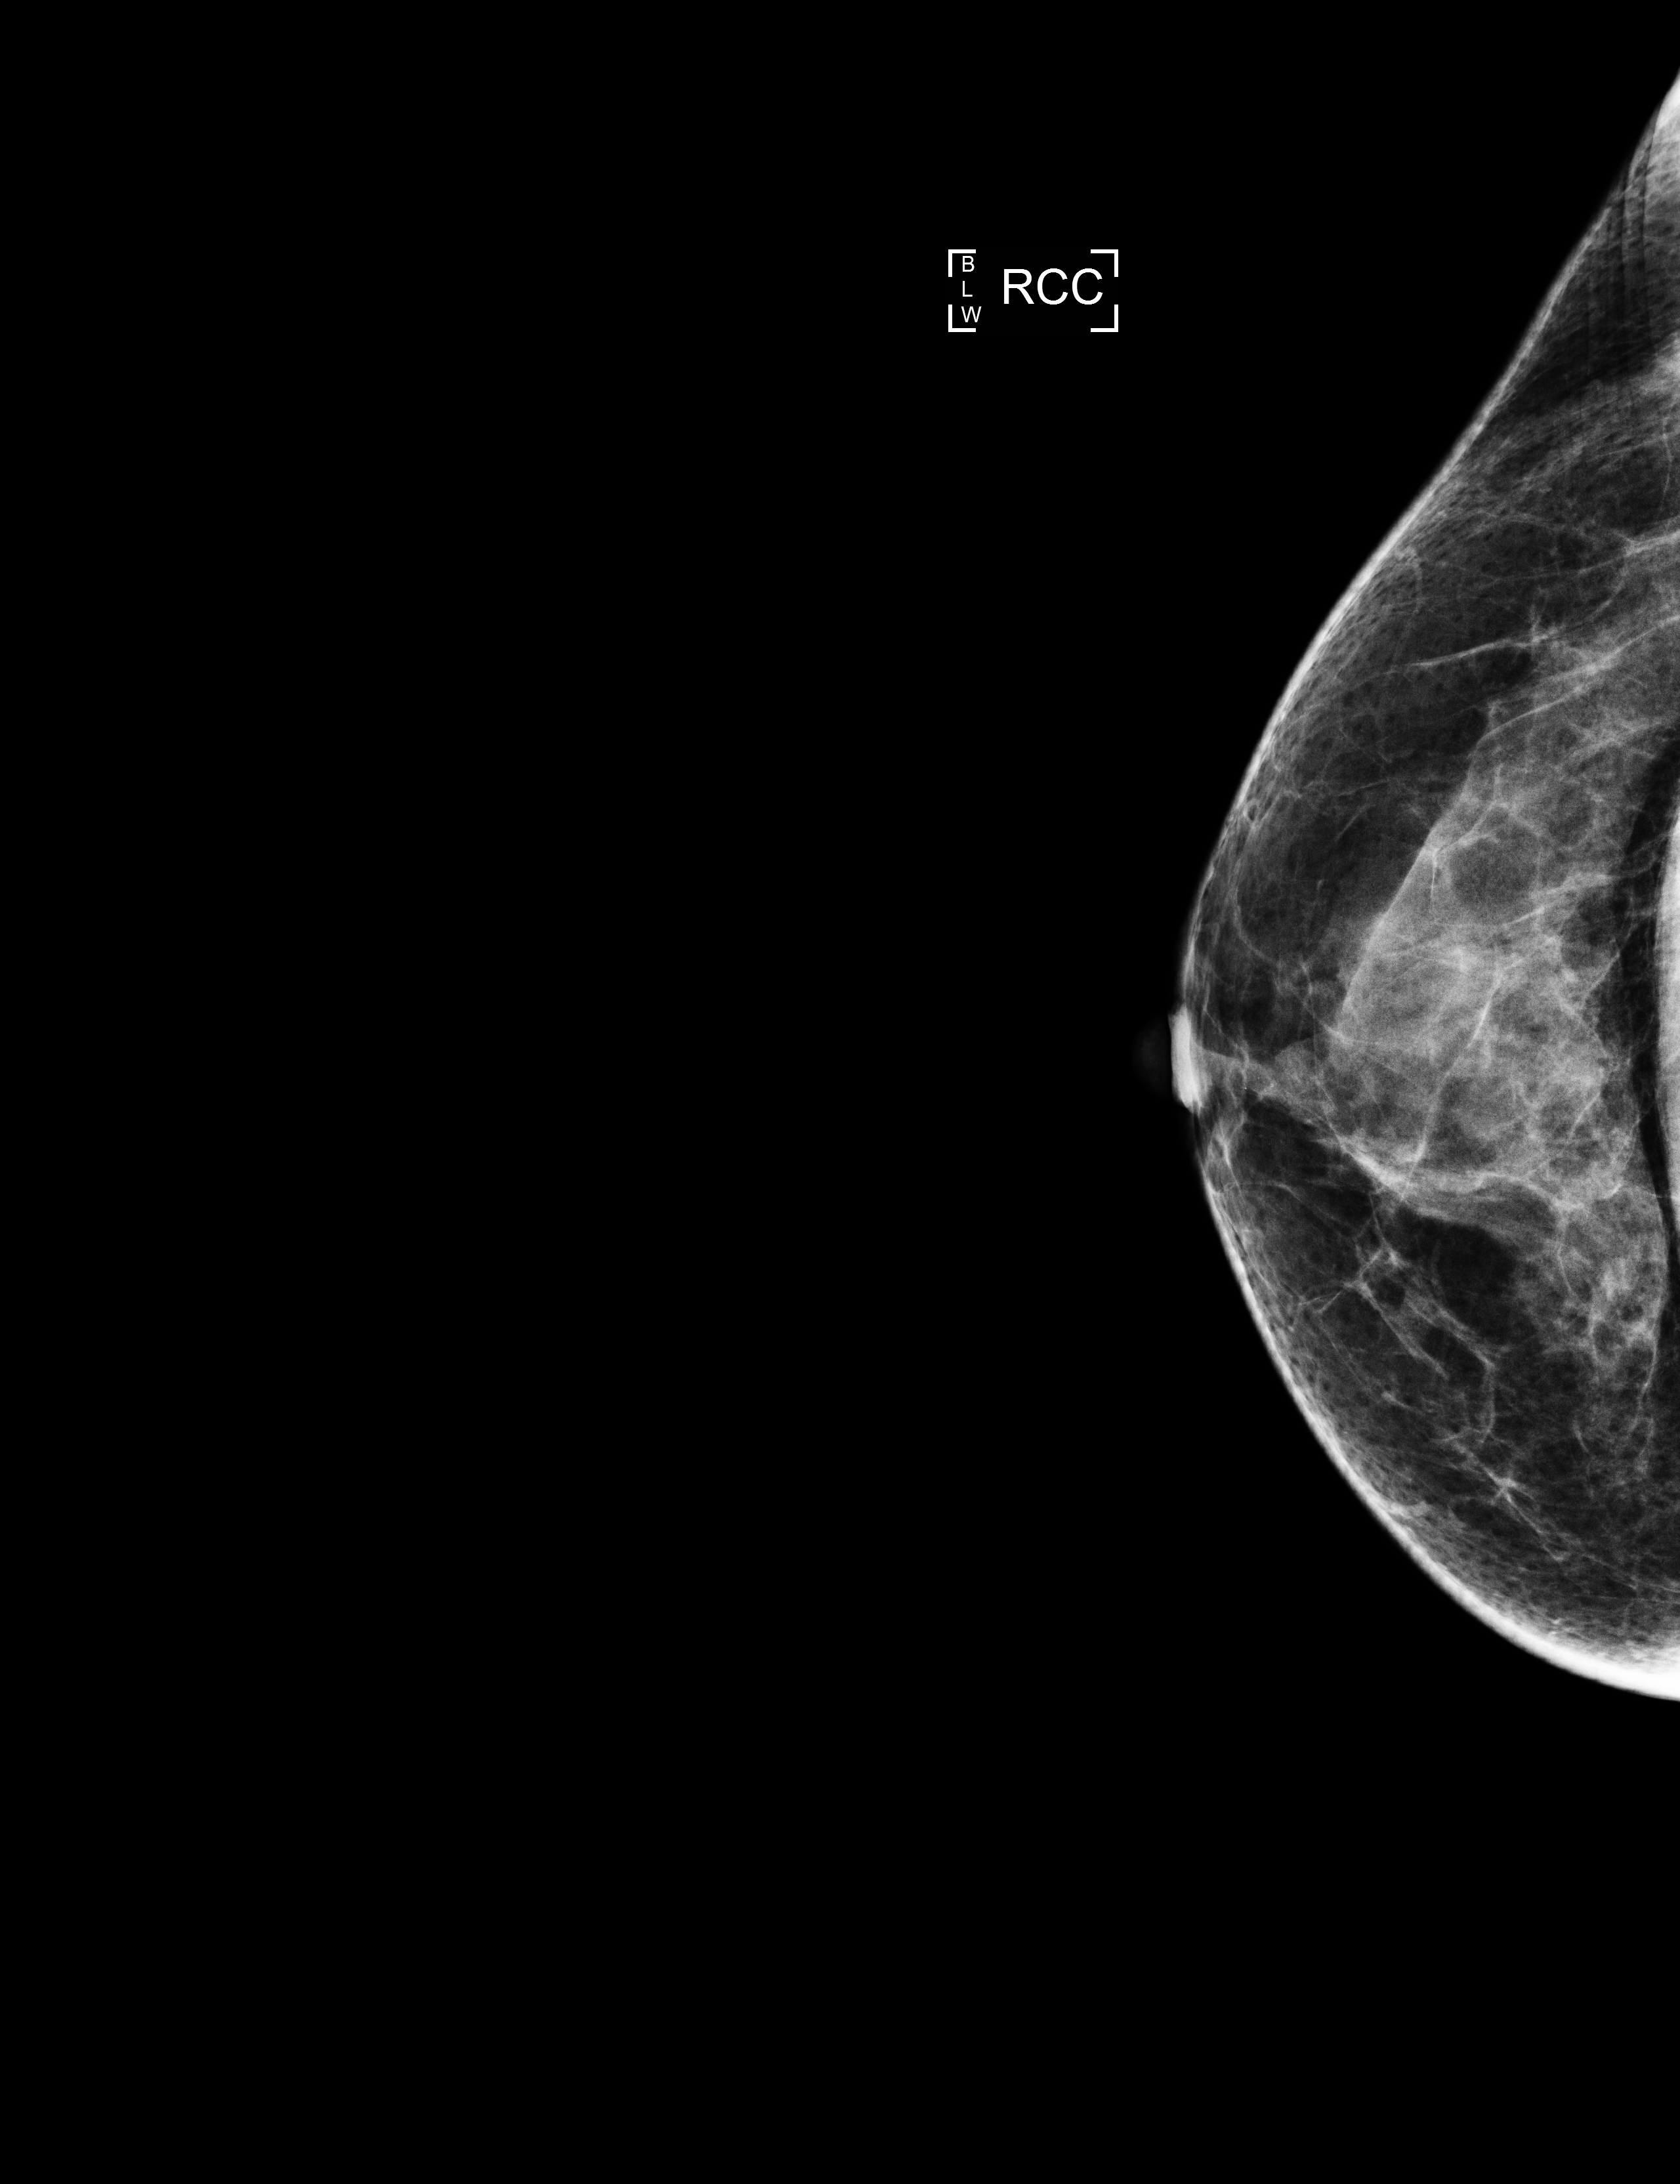
Screening examination. Patient: female, 58 years.
Image type: full-field digital mammogram. Breast: right. Projection: CC view.